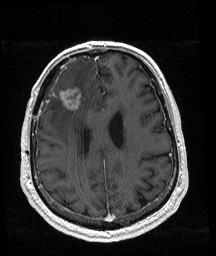
Brain MRI from a brain-tumour surgery series, one axial slice; position 67 of 192 along the scan axis; T1-weighted post-contrast; 1 mm slice thickness; 216 × 256 image matrix, field of view 211 × 250 mm. Case-level facts recorded for this patient, not image findings: histopathology: Glioblastoma; WHO grade: 4.
Annotated regions visible in this slice (expert manual segmentation):
- tumour: bounding box [x1, y1, x2, y2] px = [64, 88, 87, 110]